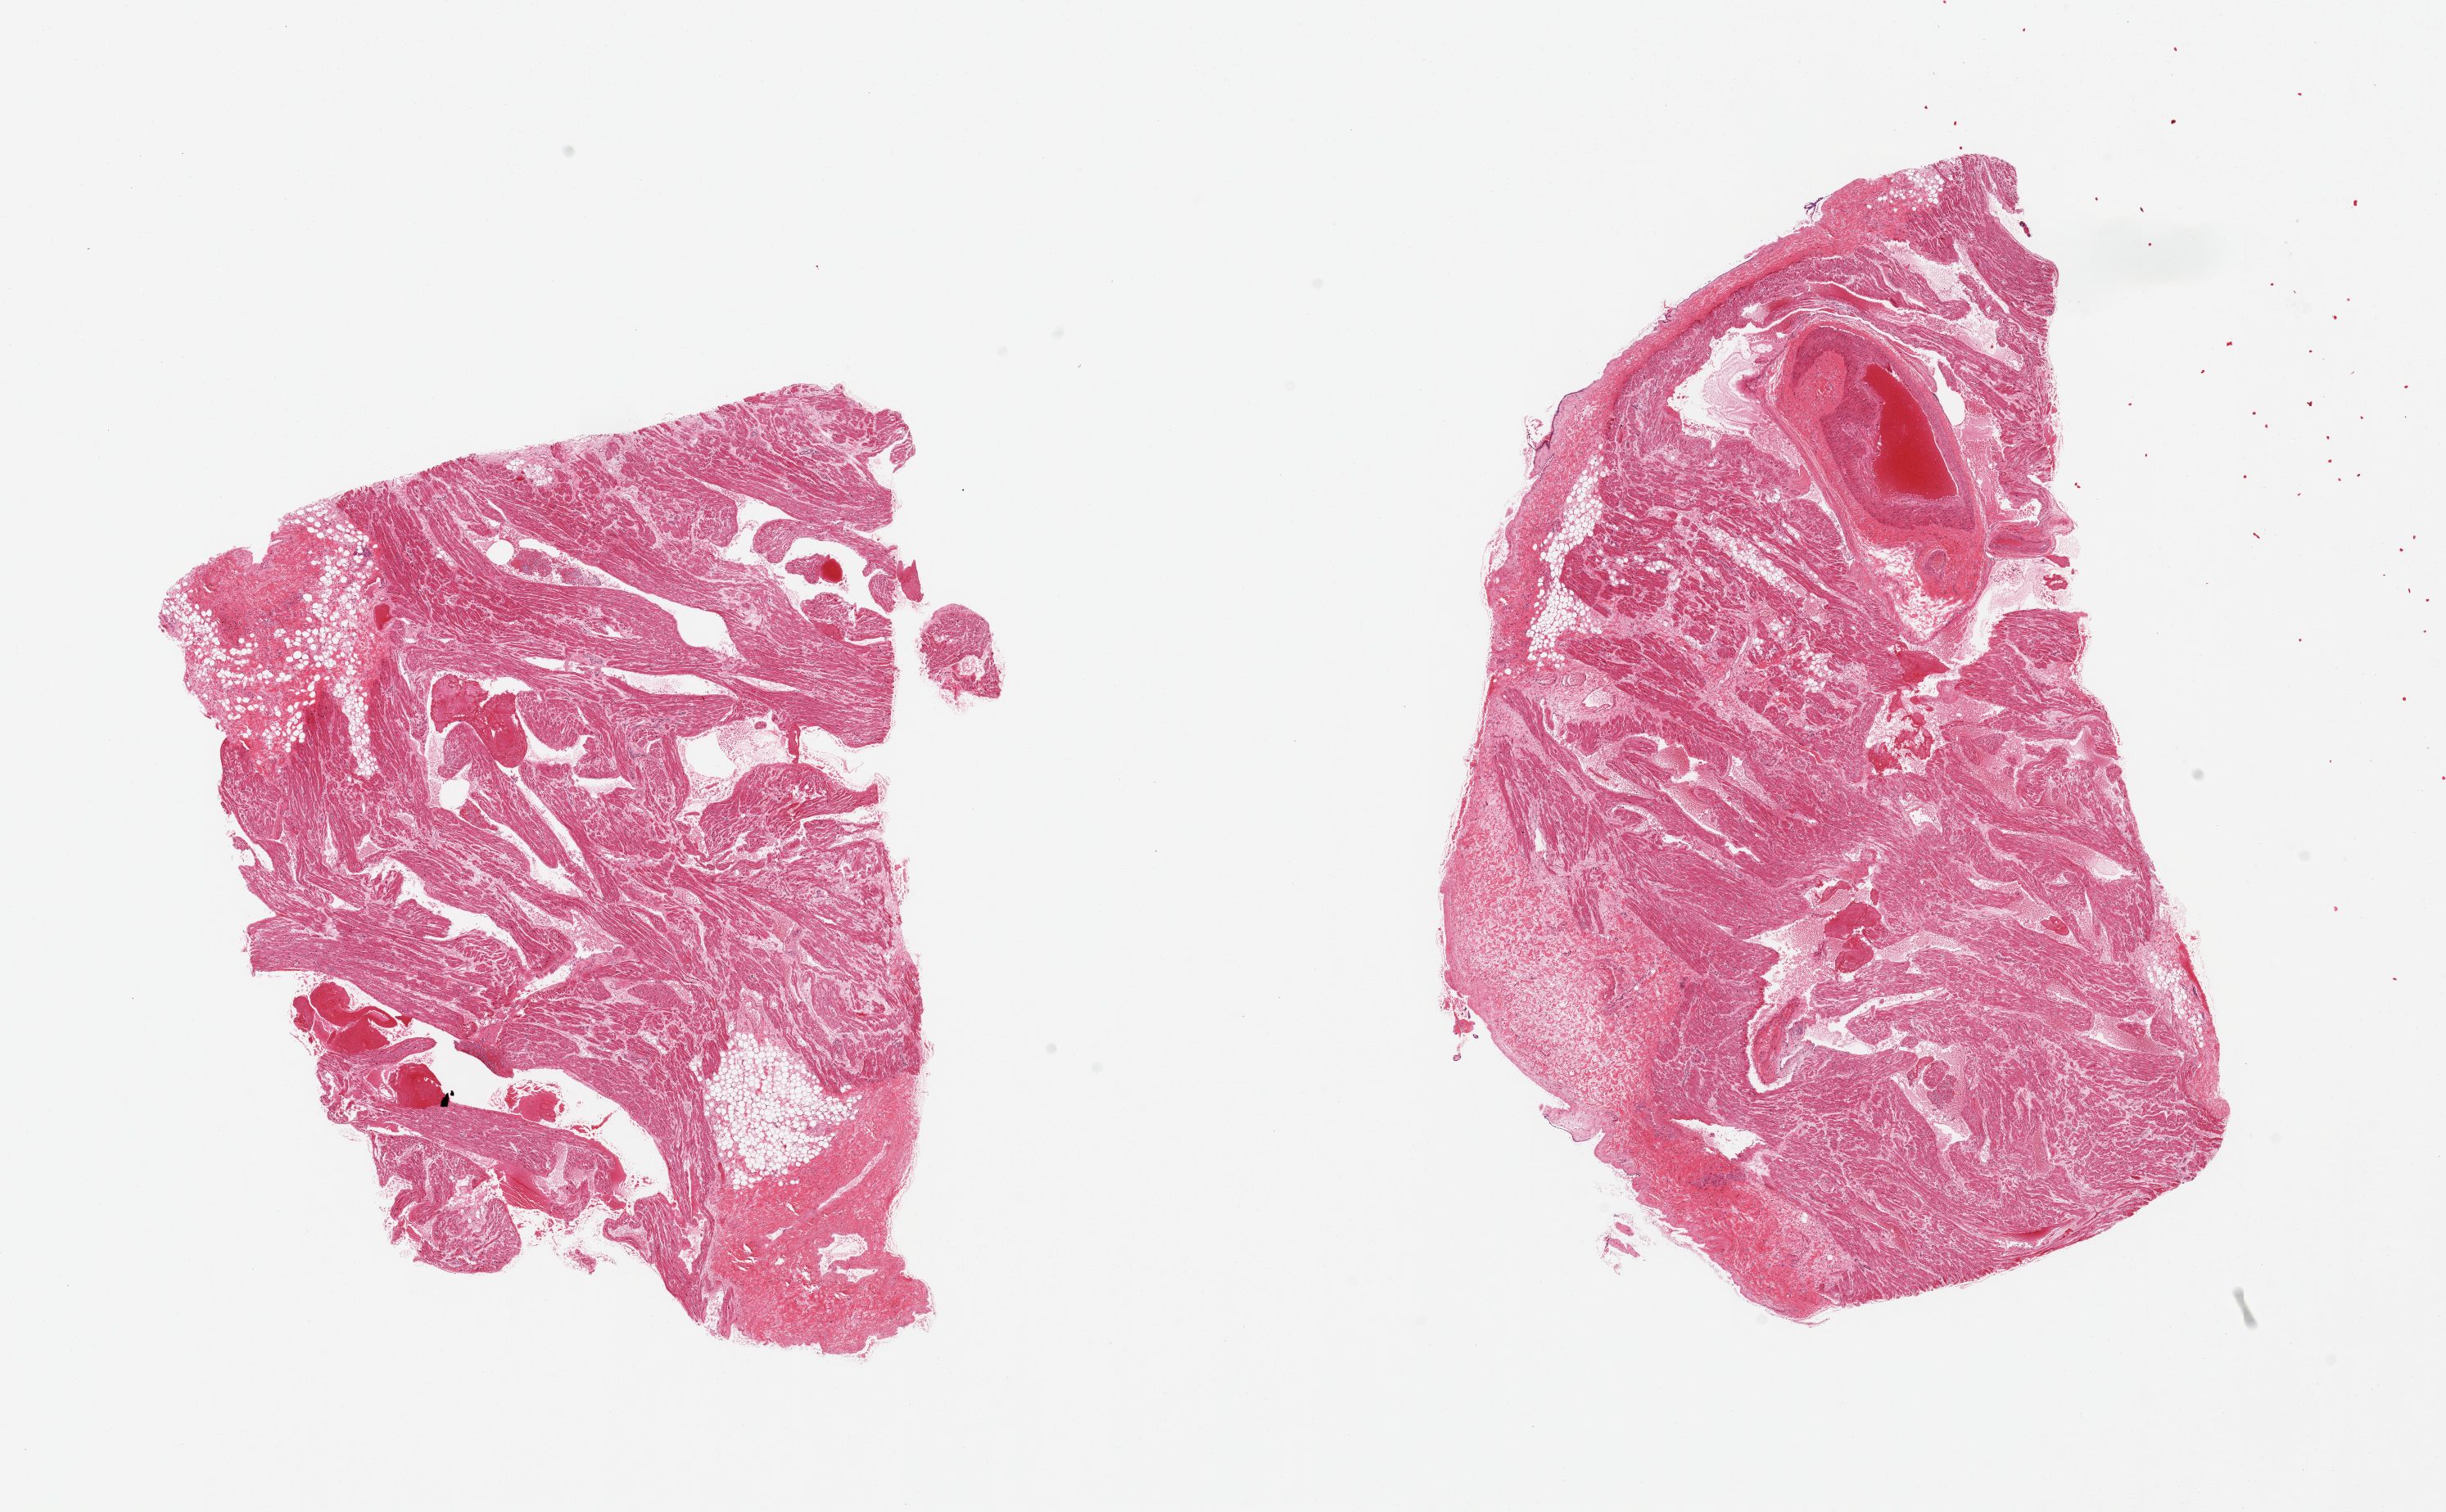
Whole-slide image, H&E stain, a low-resolution overview of the entire scanned area, about 23.6 x 14.6 mm; PAXgene-fixed, paraffin-embedded tissue; section of auricular appendage (target tissue); donor tissue sample. Female donor.
Review note (as recorded): 2 pieces, no abnormalities.